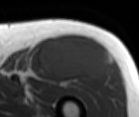
MRI of an extremity soft-tissue mass, one axial slice; slice 66 of 86 in the series (ordered by position); MR volume resampled by the dataset authors to the PET/CT grid (not the native acquisition matrix); 3.27 mm slice thickness; 139 × 117 image matrix, field of view 136 × 114 mm. Male patient. From the clinical record (not read from this slice): histological type: extraskeletal osteosarcoma; grade: high; site of the primary tumour: thigh.
Outlined on this slice (expert contour drawn on MRI and transferred to this co-registered scan by the dataset authors):
- gross tumour volume (mass): bounding box [x1, y1, x2, y2] px = [40, 36, 110, 81]